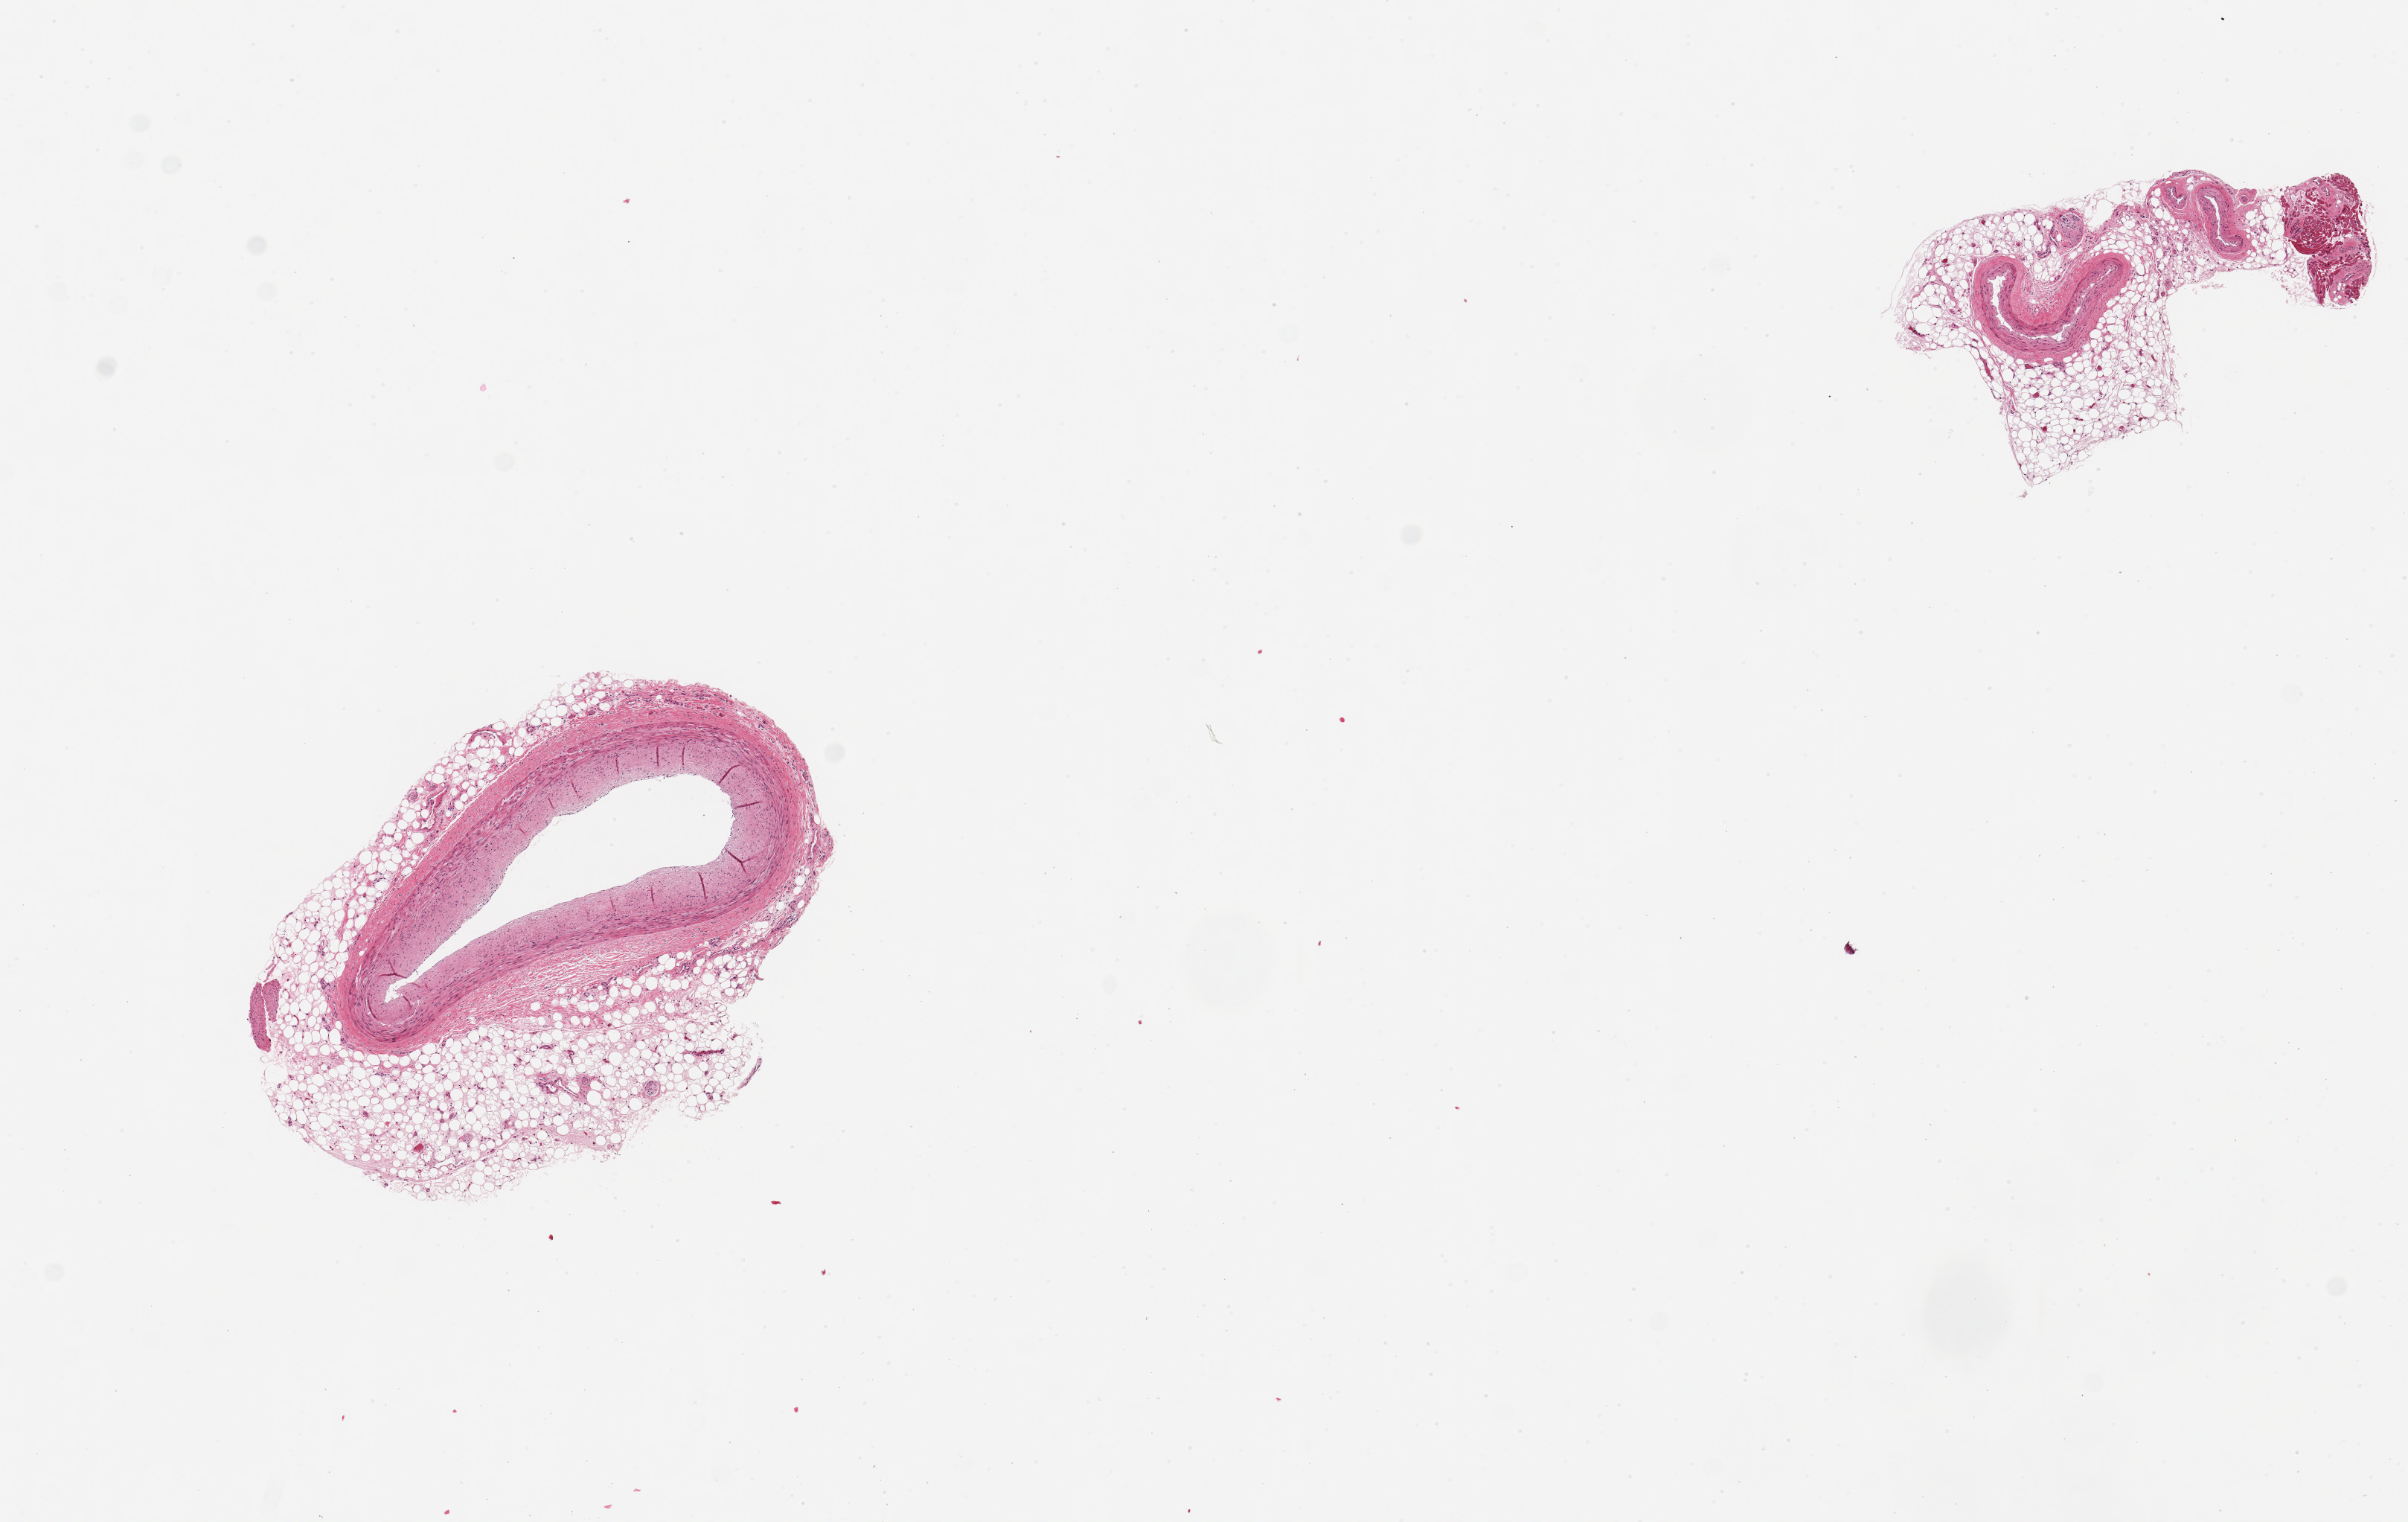
Hematoxylin and eosin (H&E) whole-slide image, brightfield — a low-resolution overview of the entire scanned area, about 12.8 x 8.1 mm (from a 20x scan); PAXgene-fixed paraffin-embedded (PFPE) section; target tissue: coronary artery; tissue donor sample. Male donor.
Reviewer comment on this tissue sample: 2 pieces, larger has up to 0.8mm perivascular fat; smaller has proportionately more fat and some myocardium.